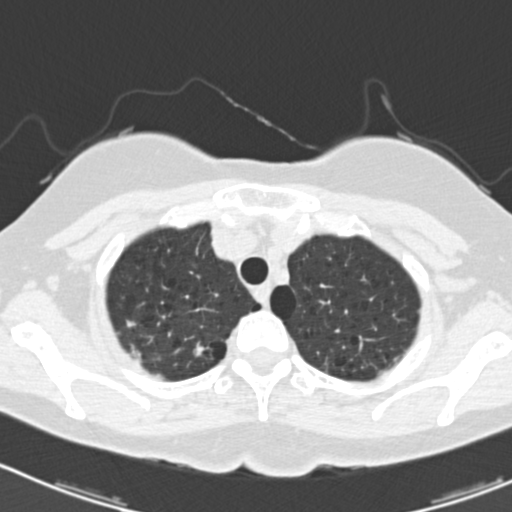
Axial slice from a low-dose chest CT screening exam. Baseline annual screen. Lung window (W 1500 / L -600 HU). 2 mm slice thickness. Standard (soft-tissue) reconstruction kernel (B30f). Slice 27 of 166 in the series. Female participant, aged 64 years at enrolment. Current smoker at enrolment.
• Expert reader's lesion annotation, bounding box [x1, y1, x2, y2] px = [180, 334, 227, 369].
• No non-calcified nodule or mass ≥4 mm was recorded by the screening reader at this exam.
• Official screen result: negative screen, minor abnormalities not suspicious for lung cancer.